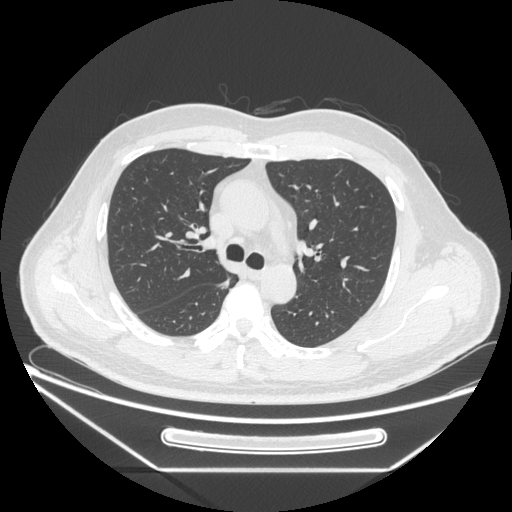
Chest CT, one axial slice. Slice 168 of 271 in the series (ordered by position). Reconstruction kernel STANDARD. 120 kVp. Lung window (W 1500 / L -600 HU). 1.25 mm slice thickness. 512 × 512 image matrix, field of view 414 × 414 mm. Male patient, age 49 years. From the clinical record (not read from this slice): clinical TNM (as recorded): T1b N0 M0; histopathological grade: G2.
Structures marked on this image (rectangle marked by the reading radiologist):
- lung tumour (recorded histology: adenocarcinoma): box from (x=215, y=274) to (x=237, y=294) px